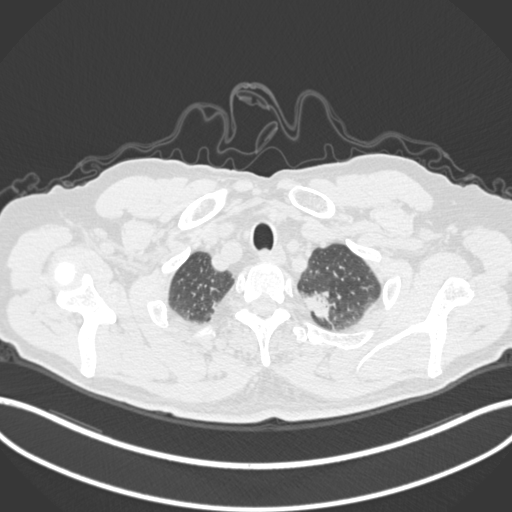
Chest CT, one axial slice; slice 290 of 306 in the series (ordered by position); 120 kVp; lung window (W 1500 / L -600 HU); 512 × 512 image matrix. Patient: male, 64 years. Case-level facts recorded for this patient, not image findings: clinical TNM (as recorded): T1c N0 M0.
Annotated regions visible in this slice (rectangle marked by the reading radiologist):
- lung tumour (recorded histology: adenocarcinoma): box from (x=301, y=283) to (x=335, y=325) px